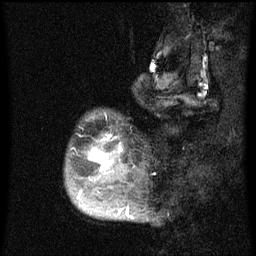
Breast MRI (dynamic contrast-enhanced), one sagittal slice. Position 13 of 60 along the scan axis. Dynamic contrast-enhanced series, image 2 of 3 at this slice position (ordered by acquisition). 1.5 T. TE 4.2 ms, TR 8 ms. 2 mm slice thickness. 256 × 256 image matrix. Female patient, age 50 years.
Annotated regions visible in this slice (semi-automatically segmented with operator editing):
- analysis volume of interest (the breast-tissue region the enhancement analysis was run in; not a lesion): box from (x=66, y=112) to (x=142, y=216) px
- tumour enhancement mask (voxels above the 70 % enhancement threshold inside the analysis volume of interest): (x=77, y=134)–(x=129, y=216)